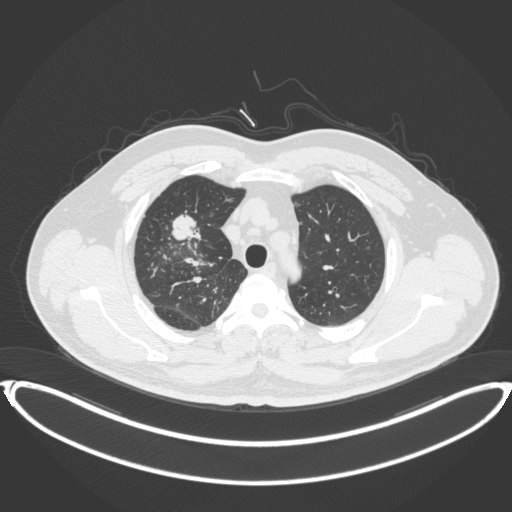
Chest CT, one axial slice. Position 304 of 399 along the scan axis. Lung window (W 1500 / L -600 HU). 1 mm slice thickness. 512 × 512 image matrix, field of view 445 × 445 mm. Male patient, age 53 years. Case-level facts recorded for this patient, not image findings: clinical TNM (as recorded): T2a N0 M0.
Outlined on this slice (rectangle marked by the reading radiologist):
- lung tumour (recorded histology: adenocarcinoma): box from (x=170, y=209) to (x=206, y=243) px